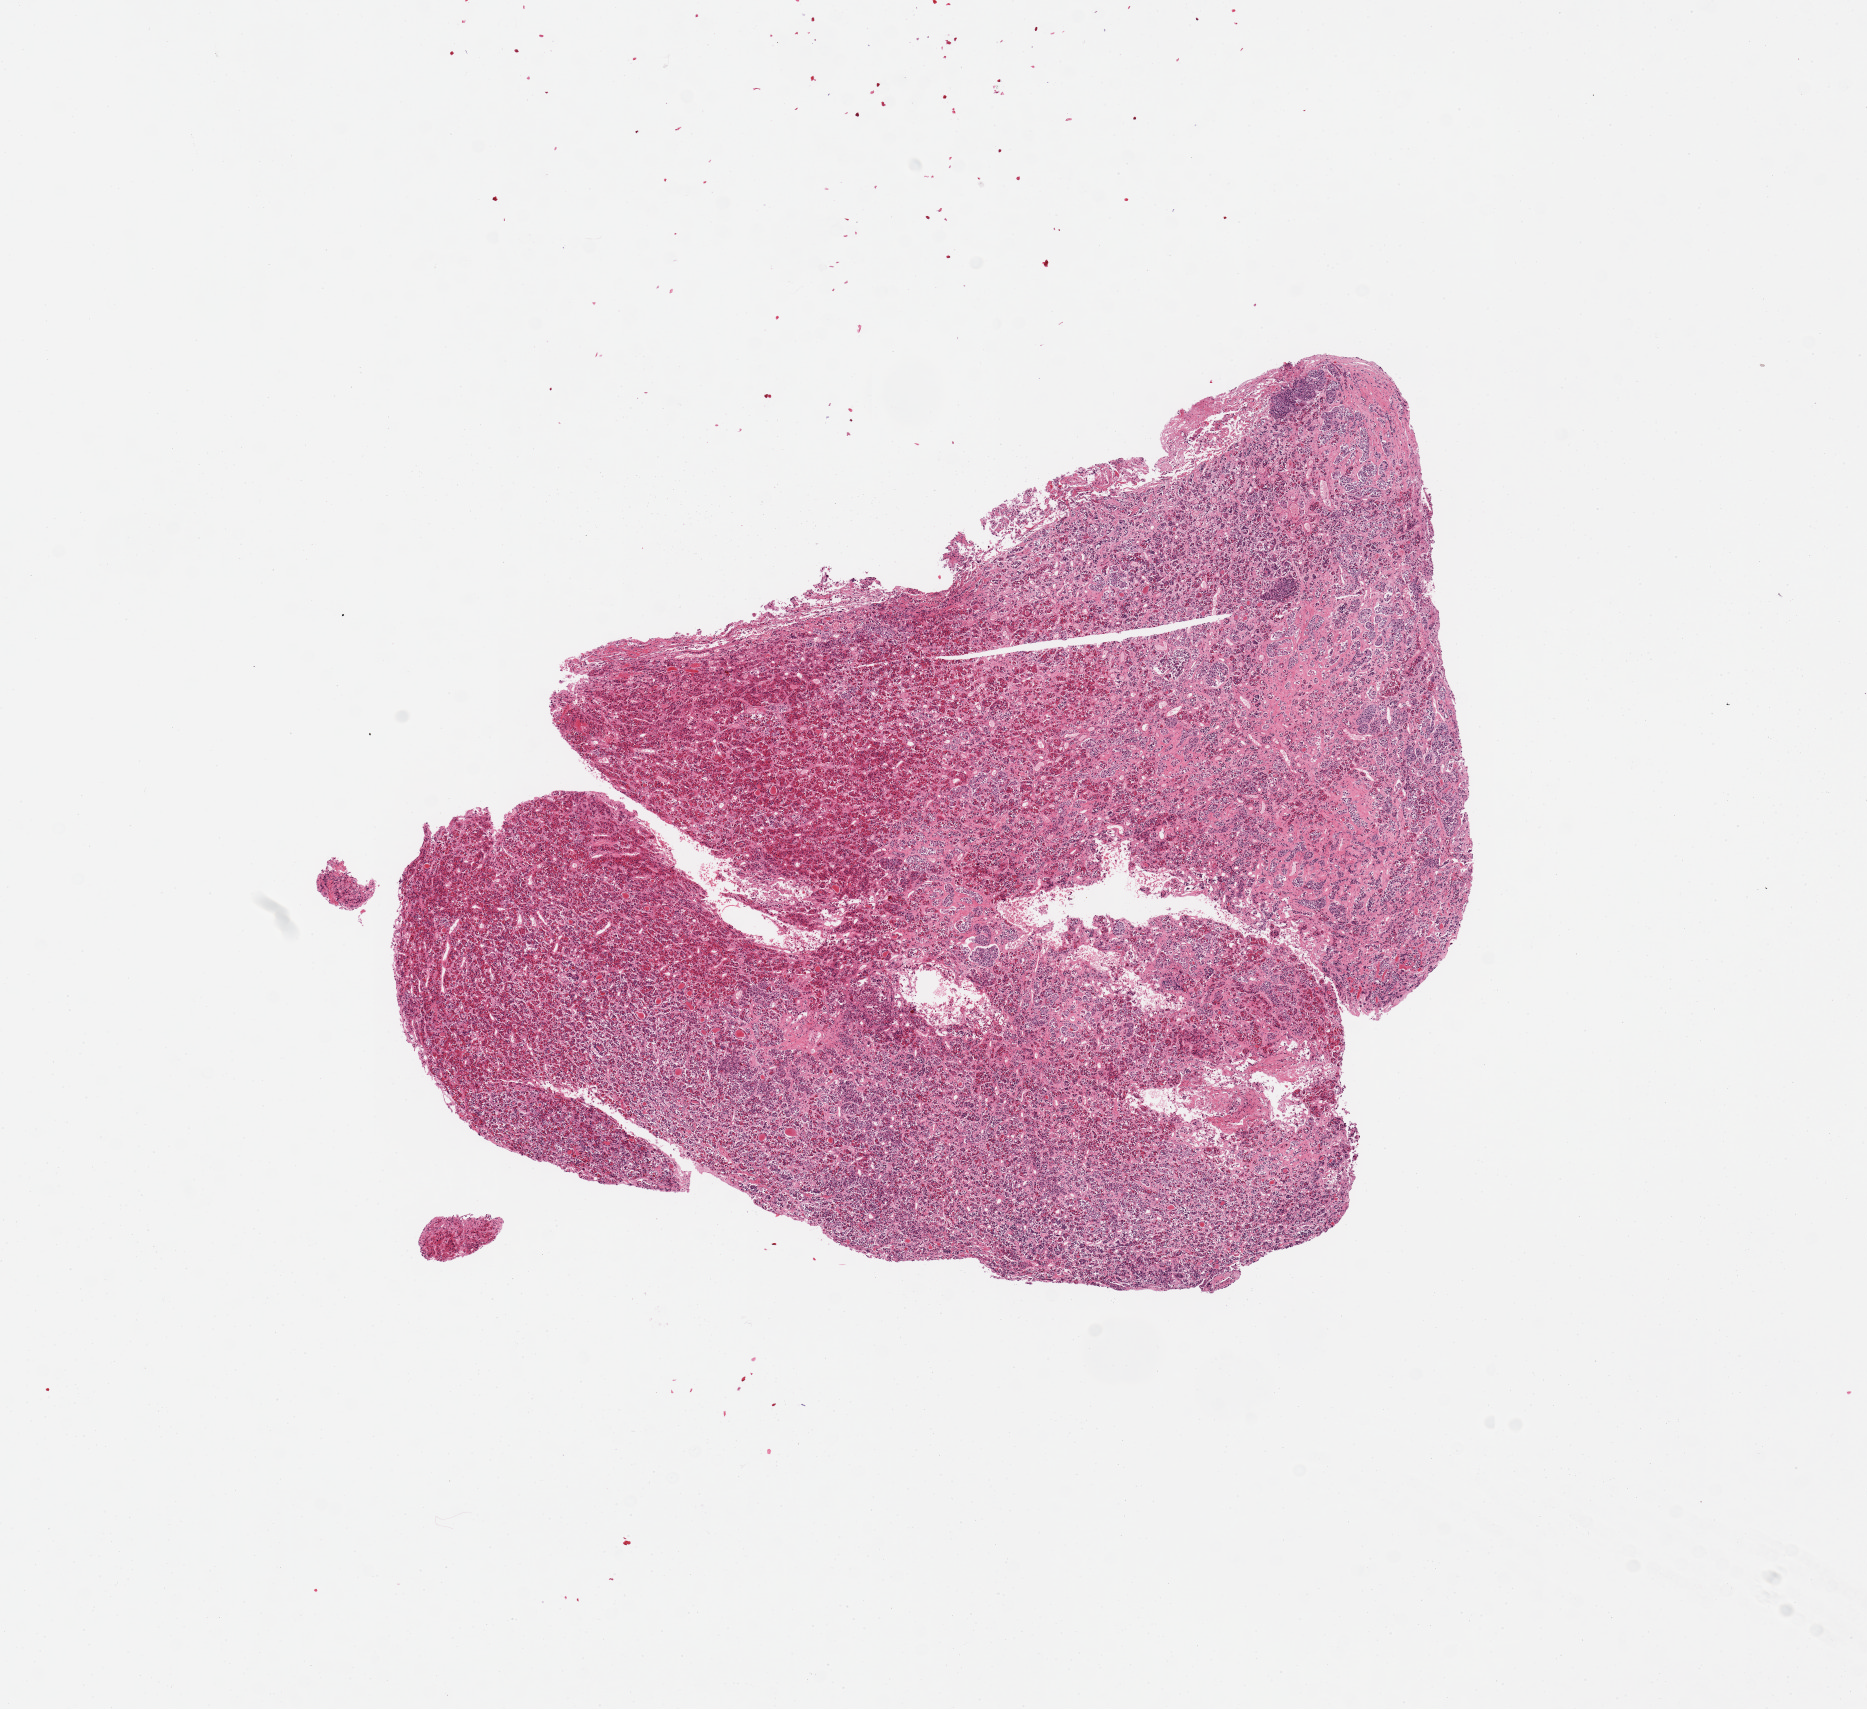
Whole-slide image, hematoxylin and eosin (H&E) stain — low-resolution overview of the scanned area, about 14.8 x 13.5 mm; PAXgene-fixed, paraffin-embedded tissue; sampled site (target tissue): pituitary; tissue donor sample. Female donor.
Pathologist's review note for this sample: 1 piece.